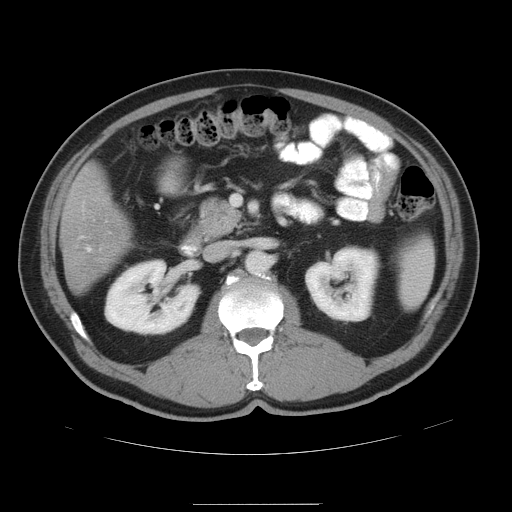
Contrast-enhanced abdominal CT, one axial slice. Slice 21 of 47 in the series (ordered by position). 120 kVp. Soft-tissue window (W 400 / L 40 HU). 5 mm slice thickness. 512 × 512 image matrix, field of view 420 × 420 mm. Male patient, age 61 years. From the clinical record (not read from this slice): diagnosis: colorectal cancer liver metastases, imaged before liver resection; multiple liver metastases: no; largest metastasis: 1.2 cm; chemotherapy before resection: yes.
Annotated regions visible in this slice (outlined manually by an expert reader):
- hepatic veins: box from (x=88, y=247) to (x=91, y=250) px
- liver: (x=63, y=167)–(x=129, y=289)
- planned liver remnant (the part of the liver to remain after resection): (x=66, y=168)–(x=129, y=258)